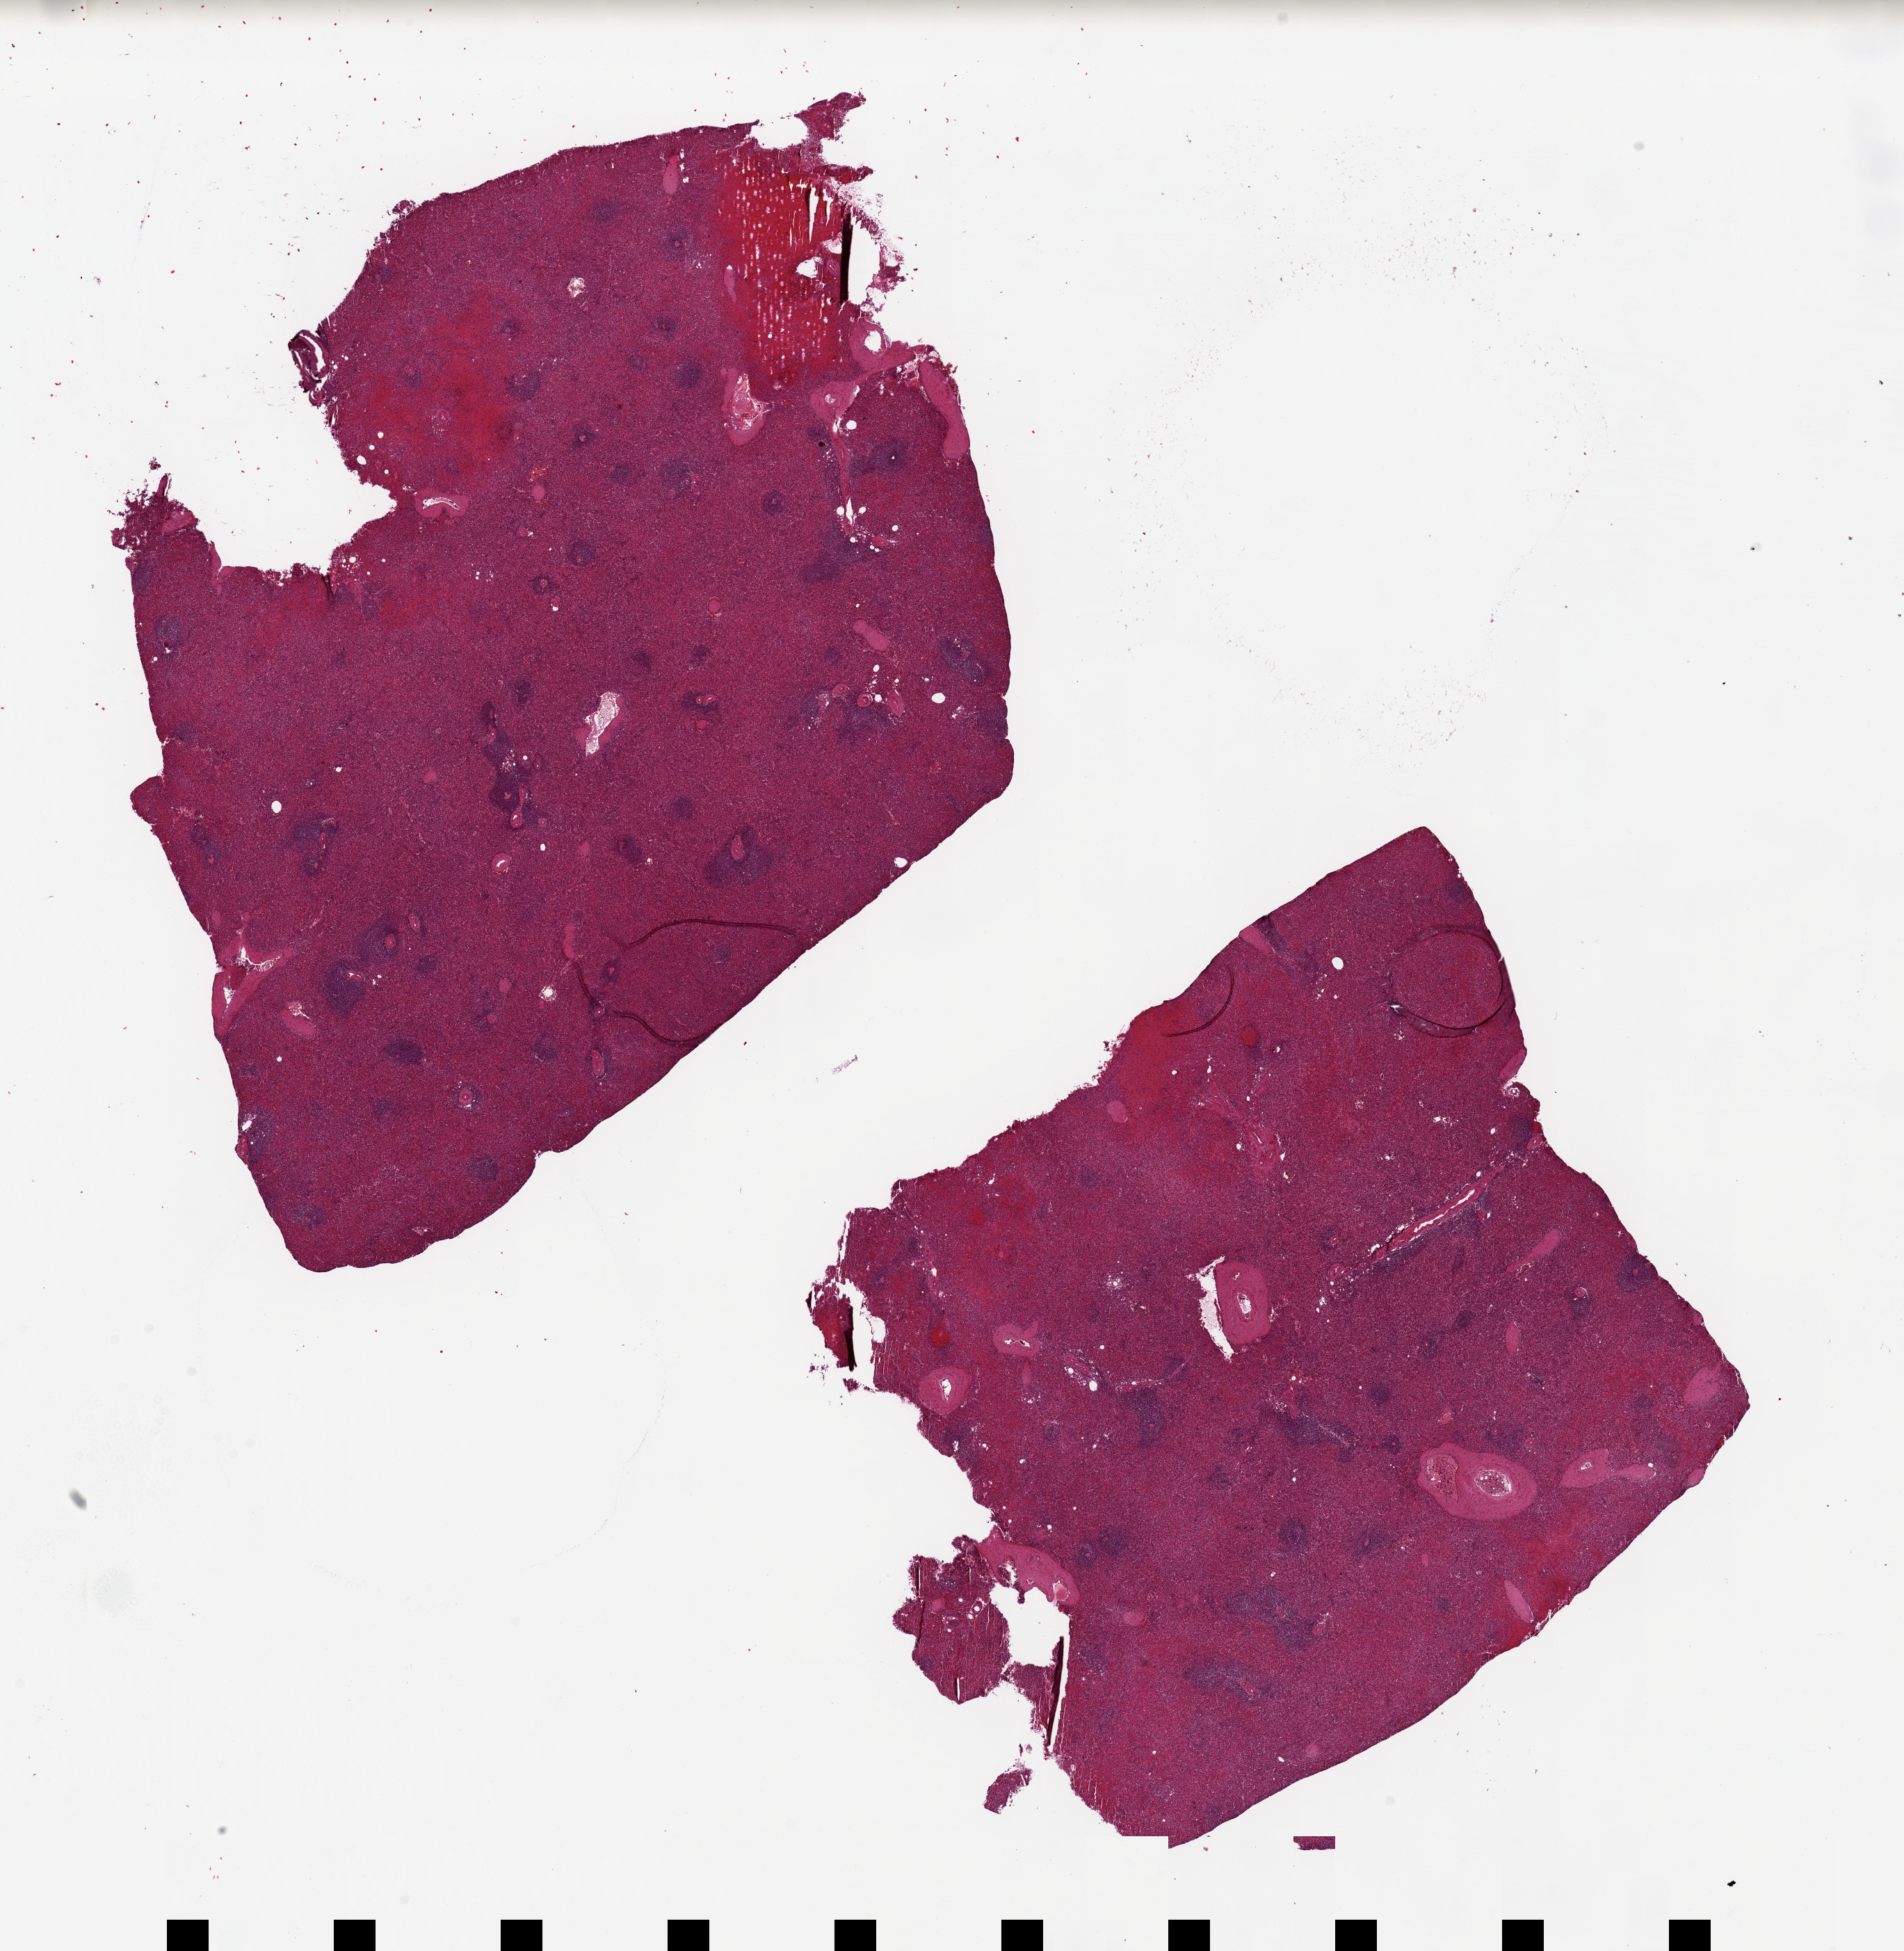
Whole-slide image, haematoxylin and eosin stain, brightfield, whole scanned area (about 21.7 x 22.2 mm) shown as a low-resolution overview. PAXgene-fixed, paraffin-embedded tissue. Target tissue: spleen. Tissue donor sample. Donor: male.
- pathologist's review note for this sample: 2 pieces, 12x10mm; & 11x9mm; moderate congestion